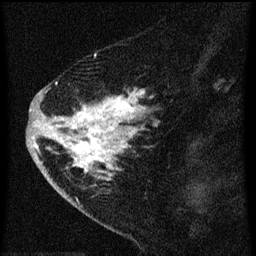
Breast MRI (dynamic contrast-enhanced), one sagittal slice; slice 21 of 60 in the series (ordered by position); dynamic contrast-enhanced series, image 2 of 3 at this slice position (ordered by acquisition); 1.5 T; TE 4.2 ms, TR 8 ms; 2 mm slice thickness; 256 × 256 image matrix. Patient: female, 47 years.
Annotated regions visible in this slice (semi-automatically segmented with operator editing):
- analysis volume of interest (the breast-tissue region the enhancement analysis was run in; not a lesion): bounding box <38,76,158,193> (left, top, right, bottom; pixels)
- tumour enhancement mask (voxels above the 70 % enhancement threshold inside the analysis volume of interest): <38,82,157,179>